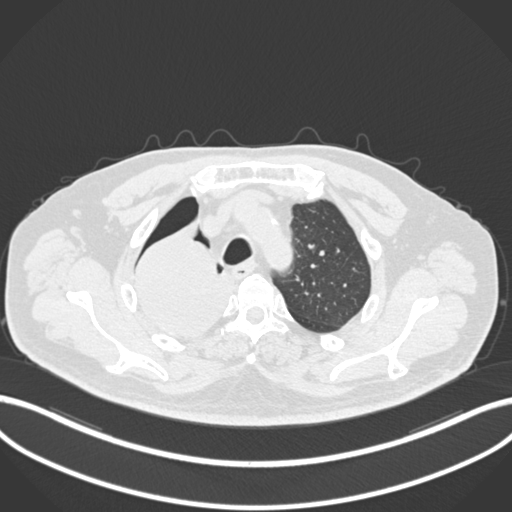
Chest CT, one axial slice; slice 170 of 218 in the series (ordered by position); reconstruction kernel B30f; 120 kVp; lung window (W 1500 / L -600 HU); 1 mm slice thickness; 512 × 512 image matrix, field of view 400 × 400 mm. Patient: male, 68 years. Case-level facts recorded for this patient, not image findings: clinical TNM (as recorded): T2a N0 M0.
Outlined on this slice (rectangle marked by the reading radiologist):
- lung tumour (recorded histology: adenocarcinoma): bounding box (x1, y1, x2, y2) in pixels: (132, 224, 241, 347)